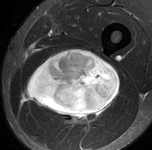
MRI of an extremity soft-tissue mass, one axial slice. Slice 63 of 90 in the series (ordered by position). STIR. MR volume resampled by the dataset authors to the PET/CT grid (not the native acquisition matrix). 3.27 mm slice thickness. 152 × 150 image matrix, field of view 148 × 146 mm. Male patient. Case-level facts recorded for this patient, not image findings: histological type: undifferentiated pleomorphic liposarcoma; grade: high; site of the primary tumour: left thigh.
Outlined on this slice (expert contour drawn on MRI and transferred to this co-registered scan by the dataset authors):
- gross tumour volume including surrounding oedema: bounding box (x1, y1, x2, y2) in pixels: (23, 48, 120, 127)
- gross tumour volume (mass): (23, 48, 120, 122)